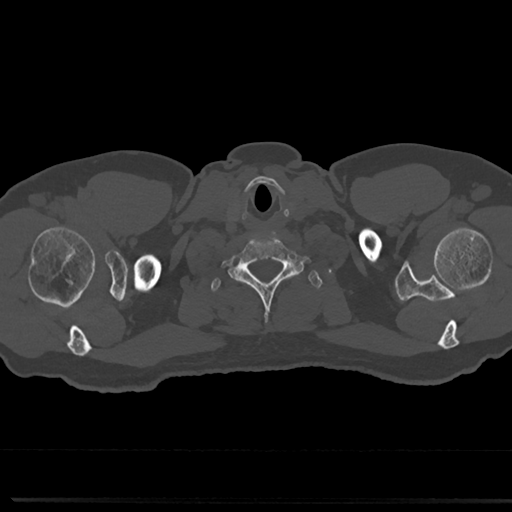
CT including the spine, one axial slice. Position 700 of 817 along the scan axis. 120 kVp. Bone window (W 1800 / L 400 HU). 512 × 512 image matrix. Male patient, age 61 years. From the clinical record (not read from this slice): primary cancer: prostate.
Annotated regions visible in this slice (semi-automatic segmentation, software-assisted and operator-edited):
- T1 vertebra: box from (x=209, y=270) to (x=319, y=296) px